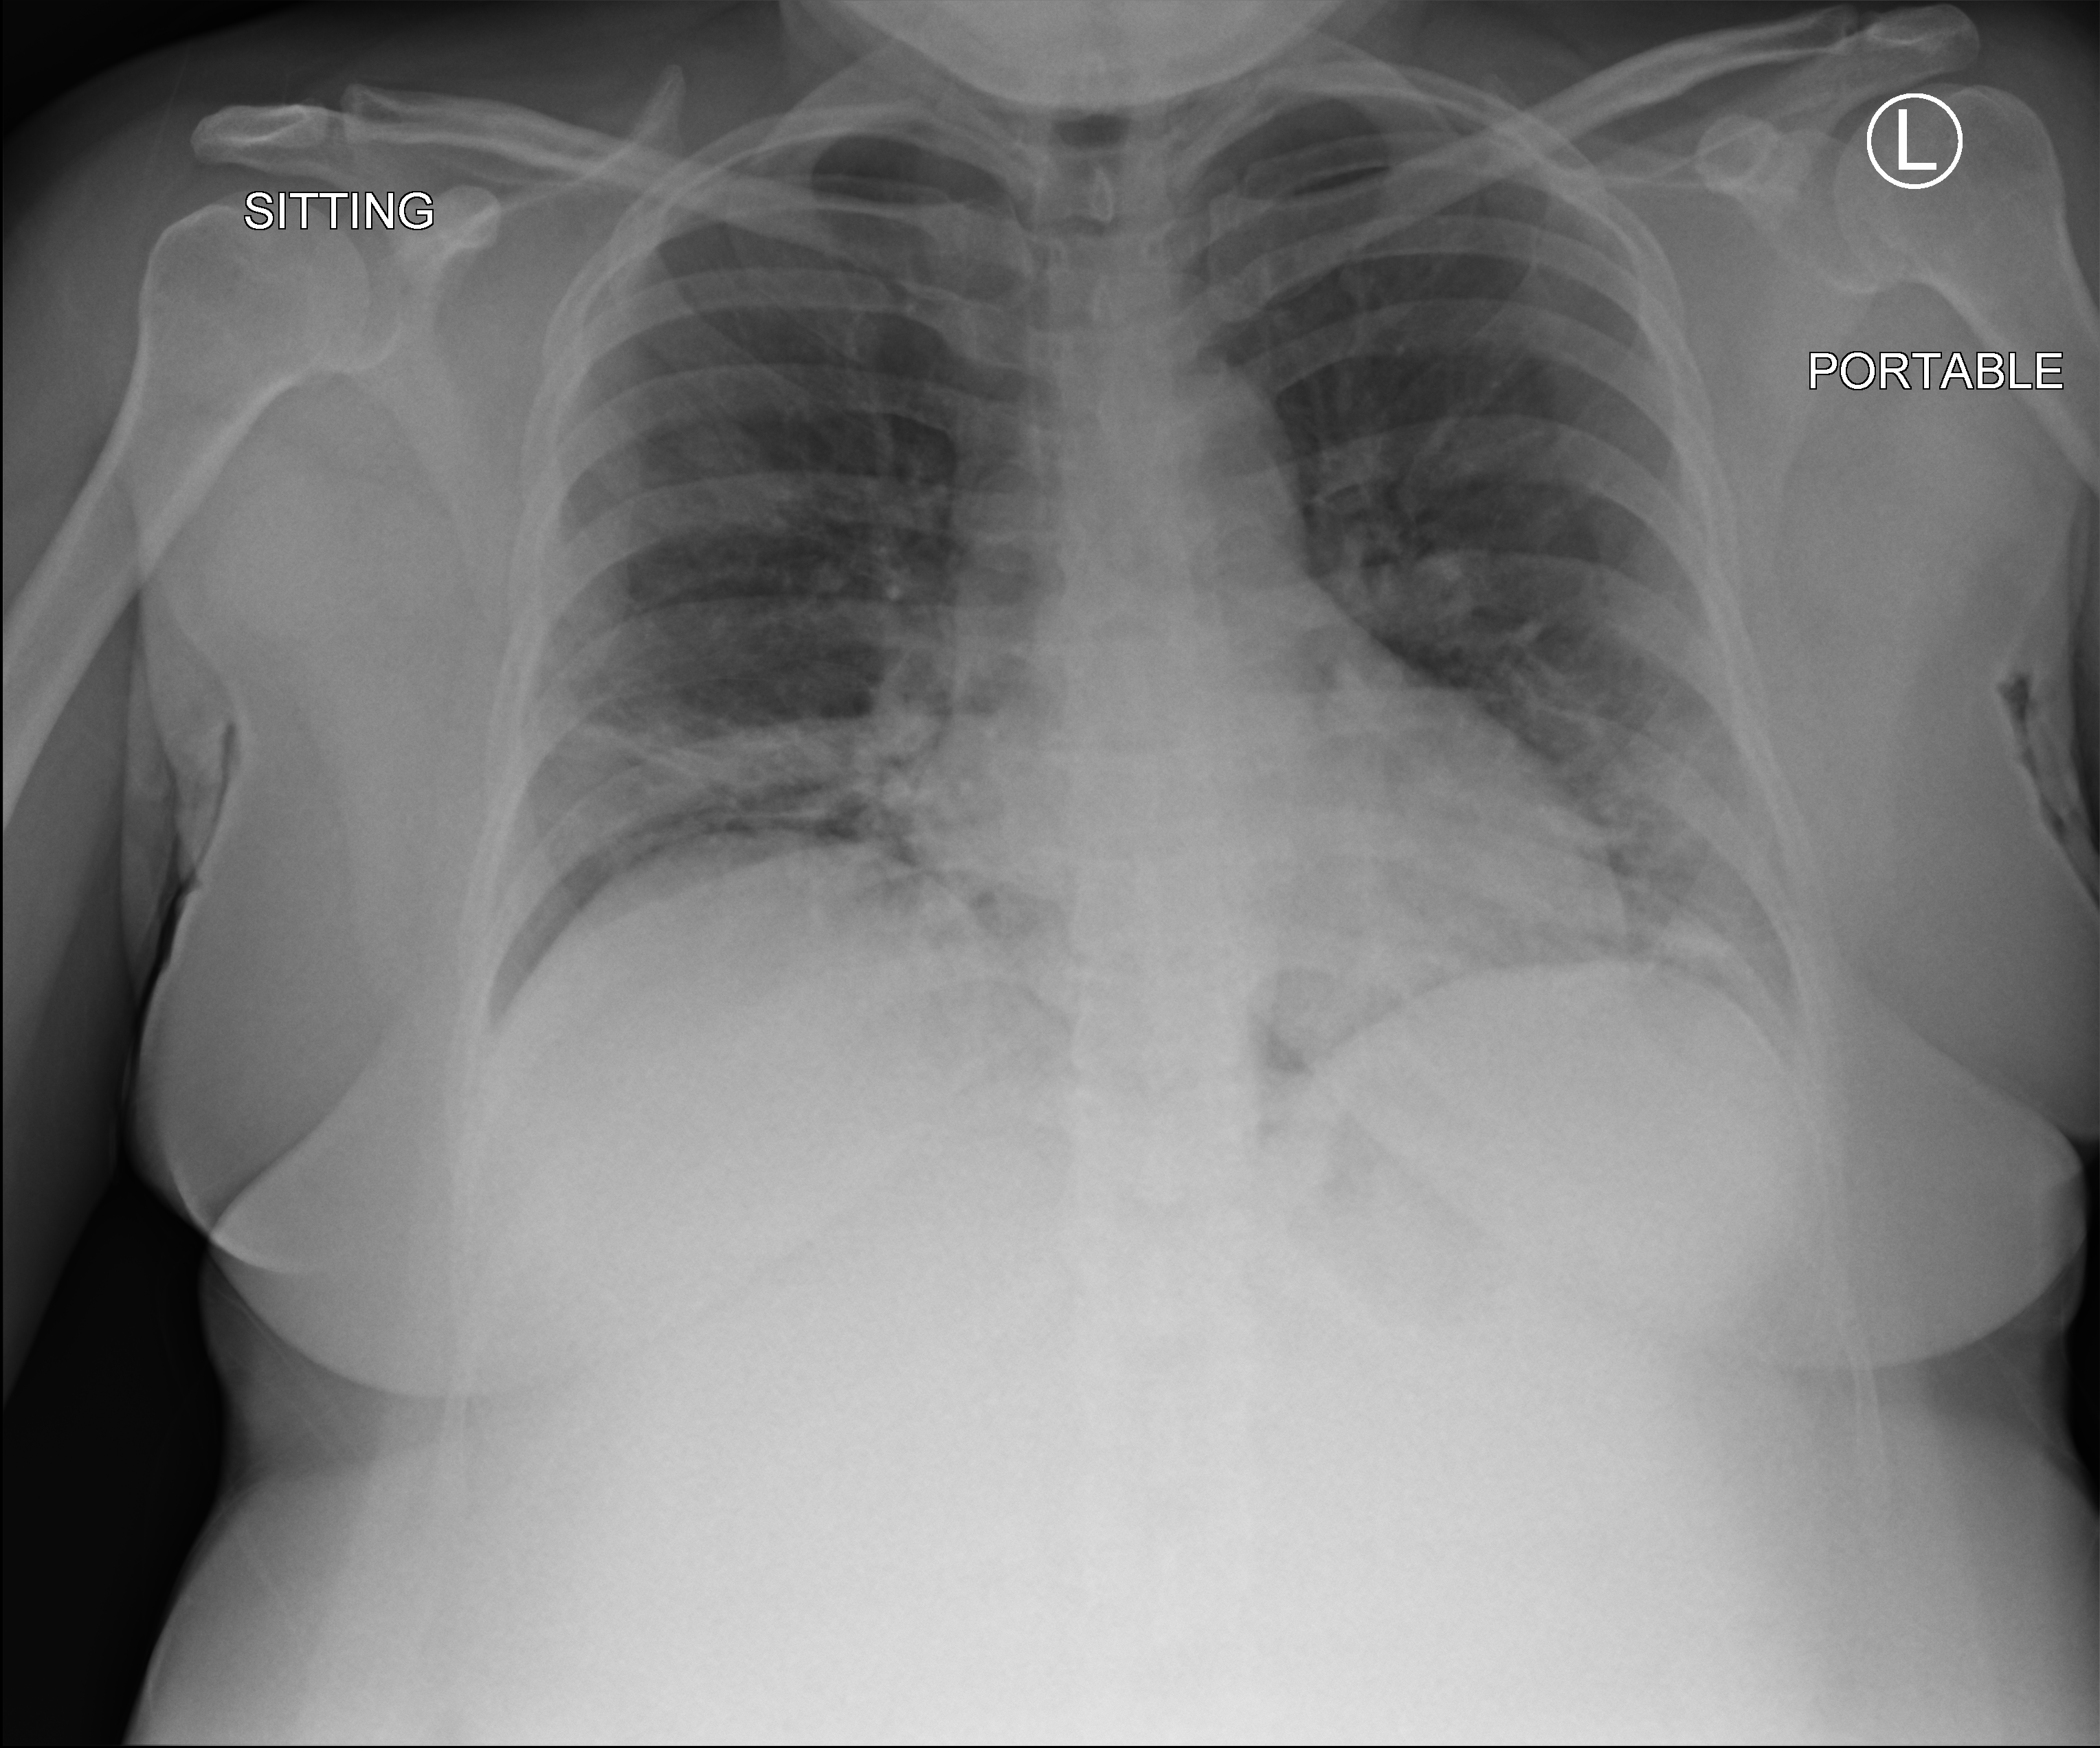
Portable chest radiograph, anteroposterior (AP) projection. Female patient hospitalised with COVID-19, age 18–59 years.
From the hospital-stay record, not from the radiograph (when in the stay this image was taken is not recorded):
- mechanically ventilated during this hospital stay: no